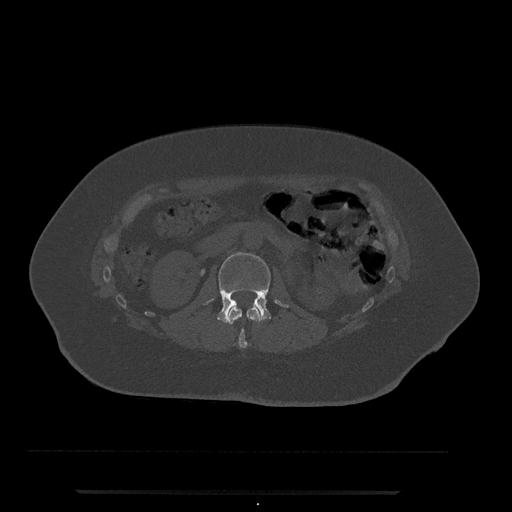
CT including the spine, one axial slice. Slice 58 of 797 in the series (ordered by position). Reconstruction kernel Br40s/3. 120 kVp. Bone window (W 1800 / L 400 HU). 0.5 mm slice thickness. 512 × 512 image matrix. Female patient, age 51 years. Case-level facts recorded for this patient, not image findings: primary cancer: neuro.
Outlined on this slice (semi-automatically segmented with operator editing):
- L1 vertebra: bounding box <226,307,261,349> (left, top, right, bottom; pixels)
- L2 vertebra: <206,252,289,323>